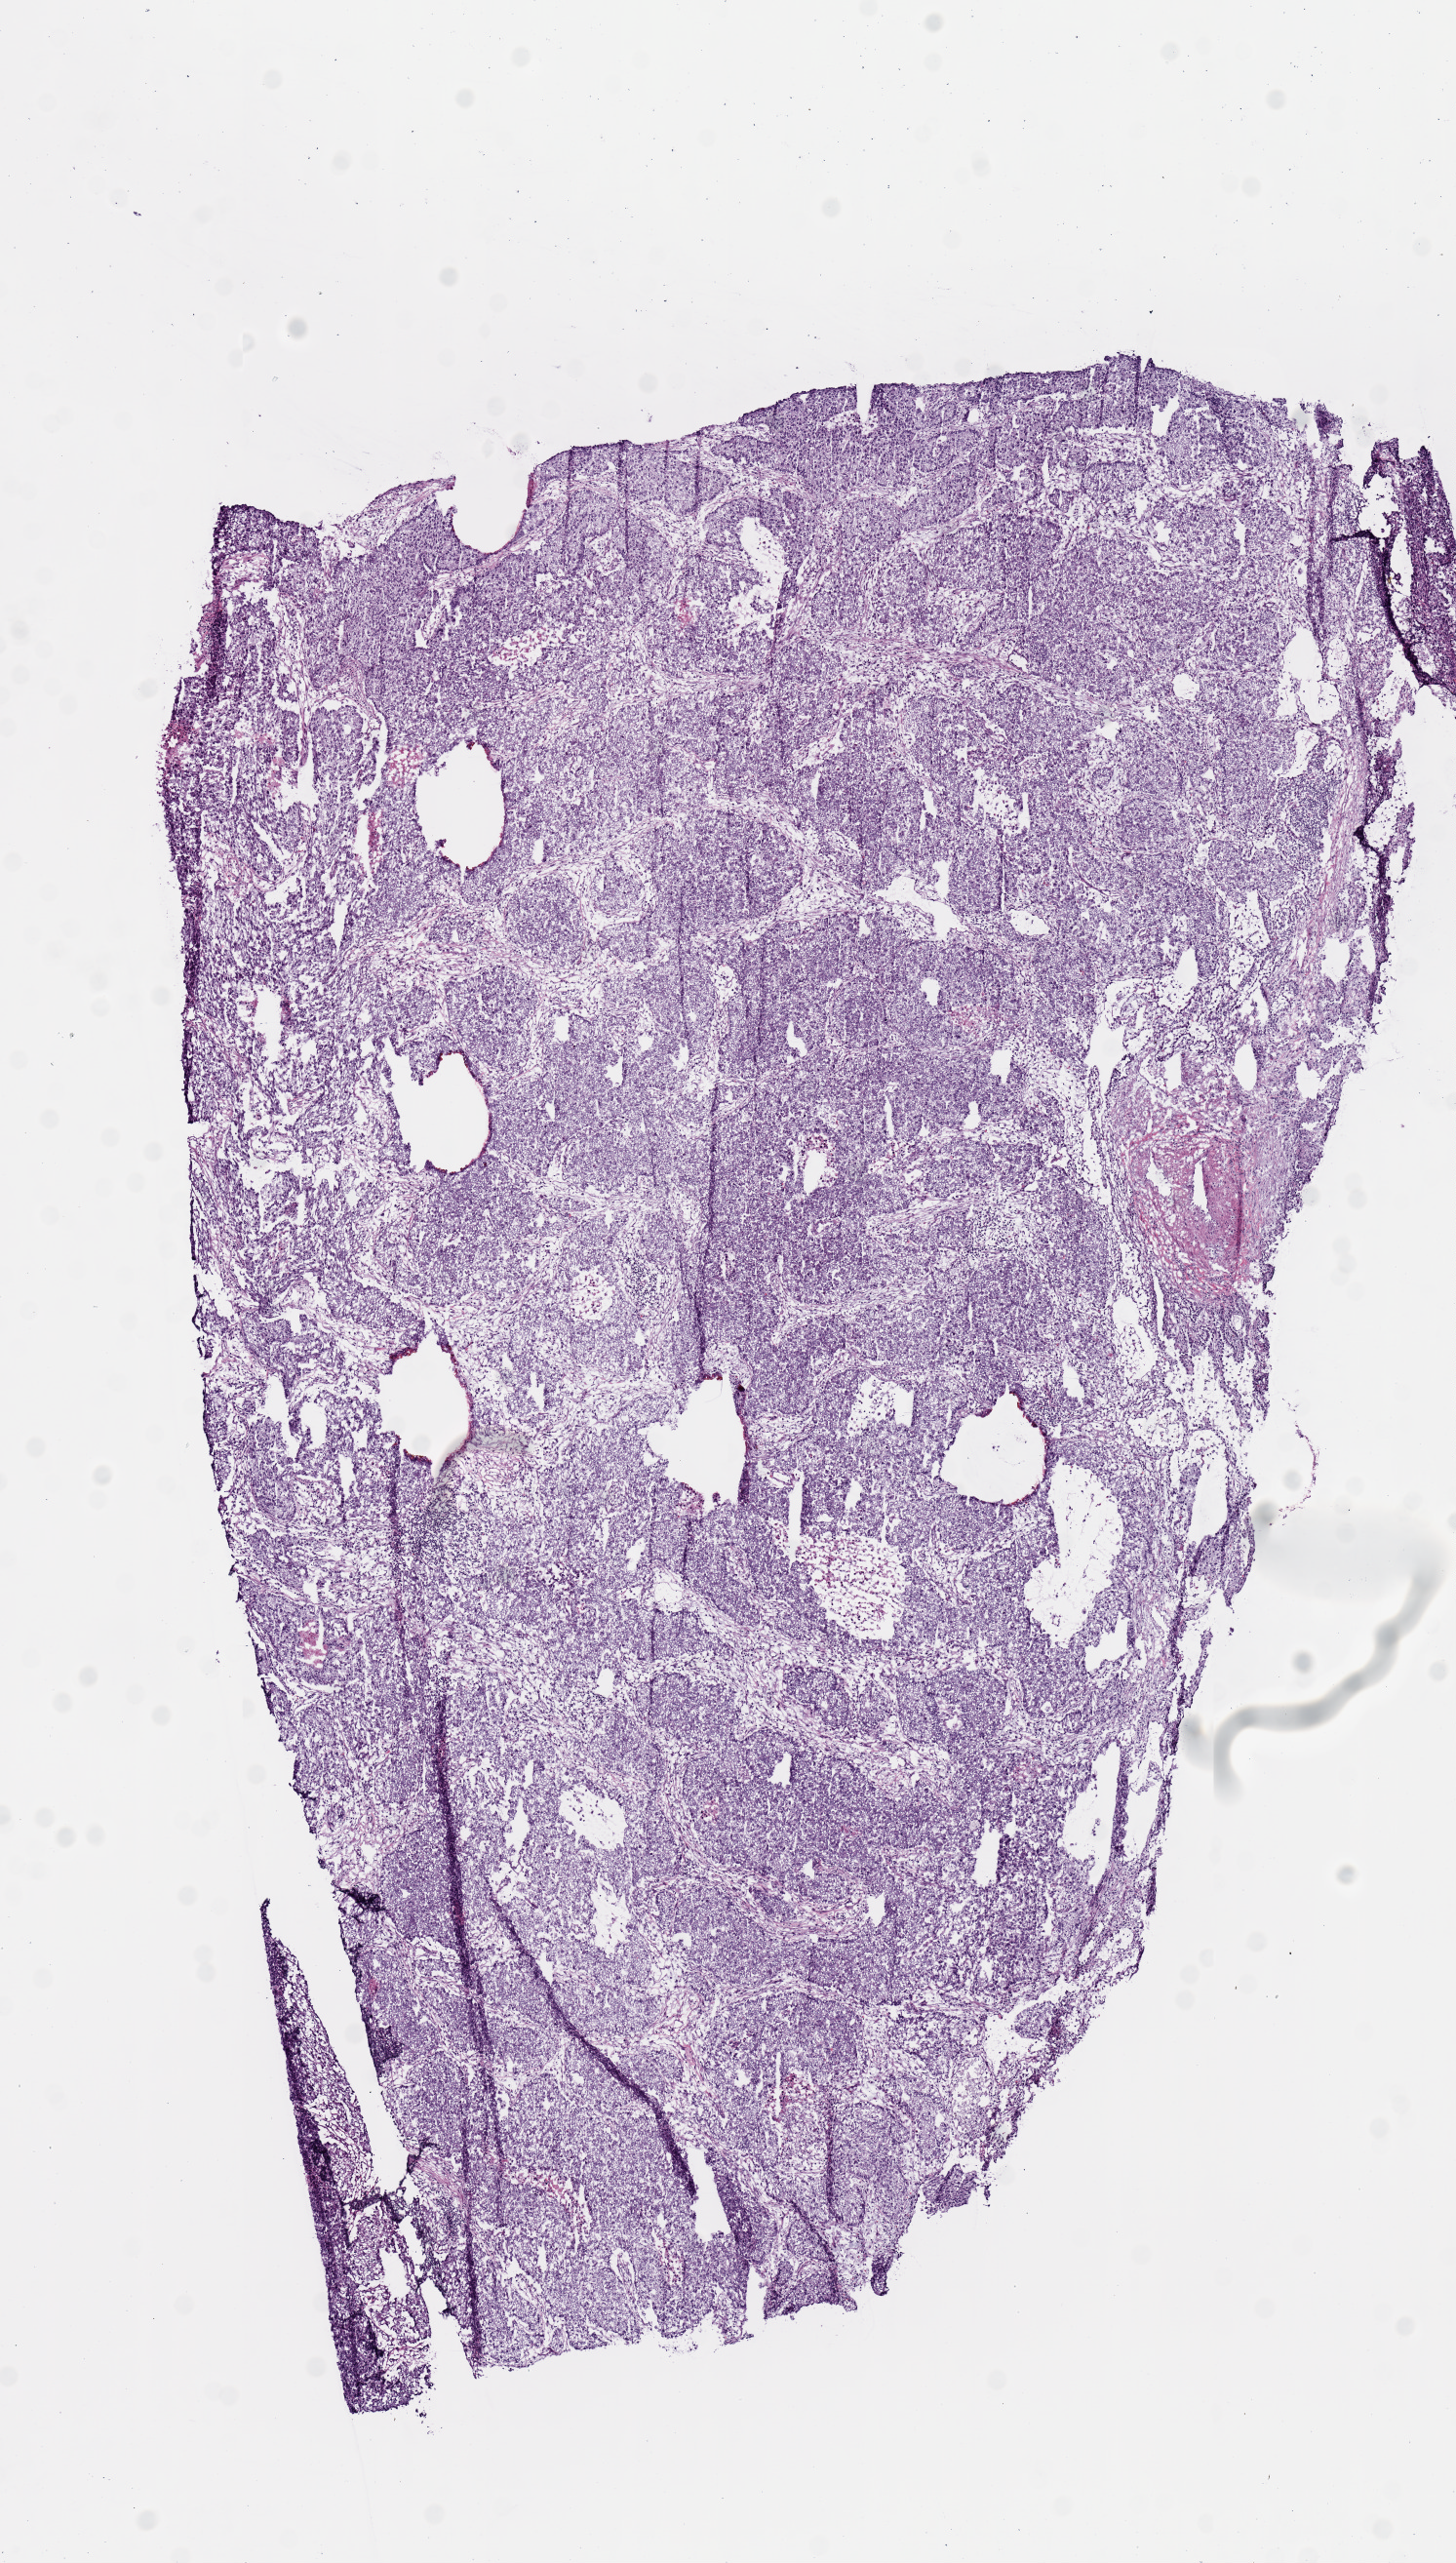
H&E whole-slide image, low-resolution overview of the scanned area, about 5.9 x 10.4 mm (from a 20x scan). Frozen section. Sample: primary tumour, lung. Female patient; age at initial diagnosis 42 years.
Pathologic diagnosis: Adenocarcinoma with mixed subtypes (middle lobe, lung).